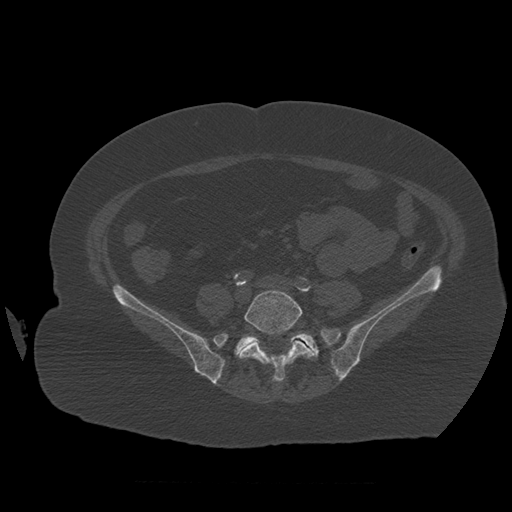
CT including the spine, one axial slice; slice 178 of 399 in the series (ordered by position); reconstruction kernel STANDARD; 120 kVp; bone window (W 1800 / L 400 HU); 512 × 512 image matrix, field of view 404 × 404 mm. Patient age 81 years. From the clinical record (not read from this slice): primary cancer: renal.
Outlined on this slice (semi-automatic segmentation, software-assisted and operator-edited):
- L5 vertebra: box from (x=240, y=290) to (x=316, y=382) px